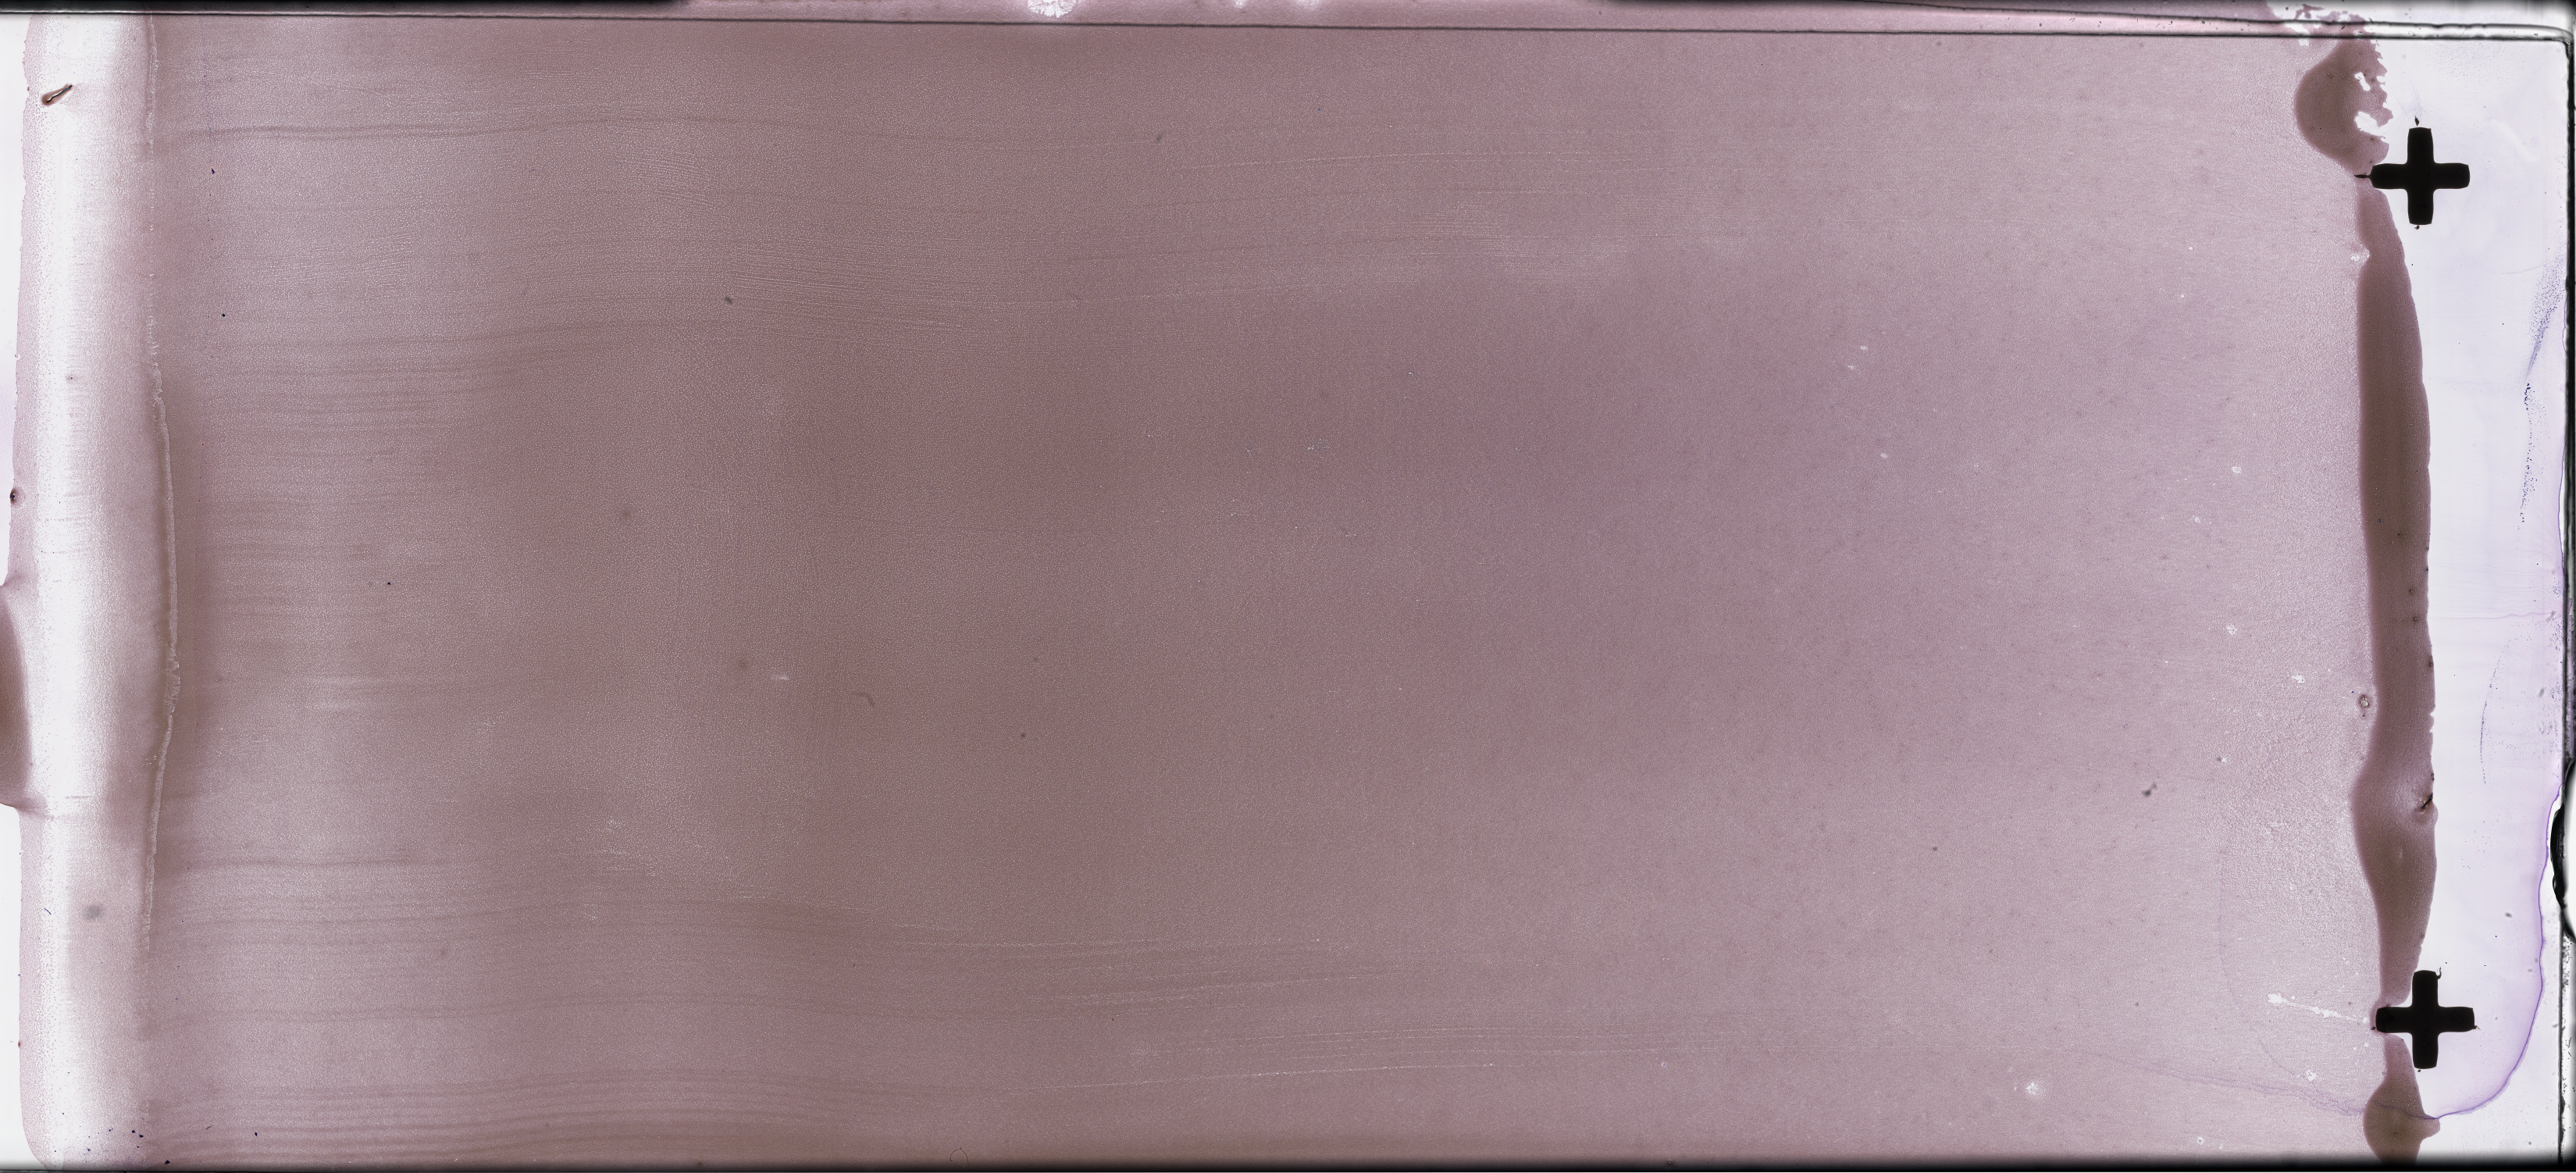
Whole-slide image of a whole blood smear, Wright-Giemsa stain, low-resolution overview of the scanned area, about 53.3 x 24.3 mm; specimen time point: collected at baseline (before treatment). Patient: male.
From a patient with: Plasma Cell Myeloma.